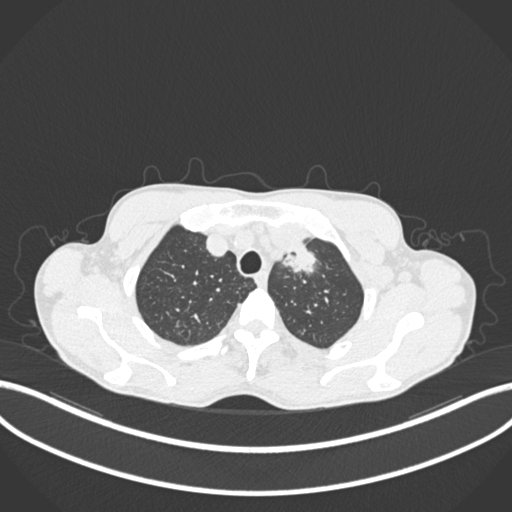
Chest CT, one axial slice; slice 174 of 211 in the series (ordered by position); 120 kVp; lung window (W 1500 / L -600 HU); 1 mm slice thickness; 512 × 512 image matrix. Patient: male, 58 years. From the clinical record (not read from this slice): clinical TNM (as recorded): T1c N1 M0.
Annotated regions visible in this slice (bounding box drawn by a radiologist):
- lung tumour (recorded histology: adenocarcinoma): bounding box (x1, y1, x2, y2) in pixels: (273, 235, 325, 278)